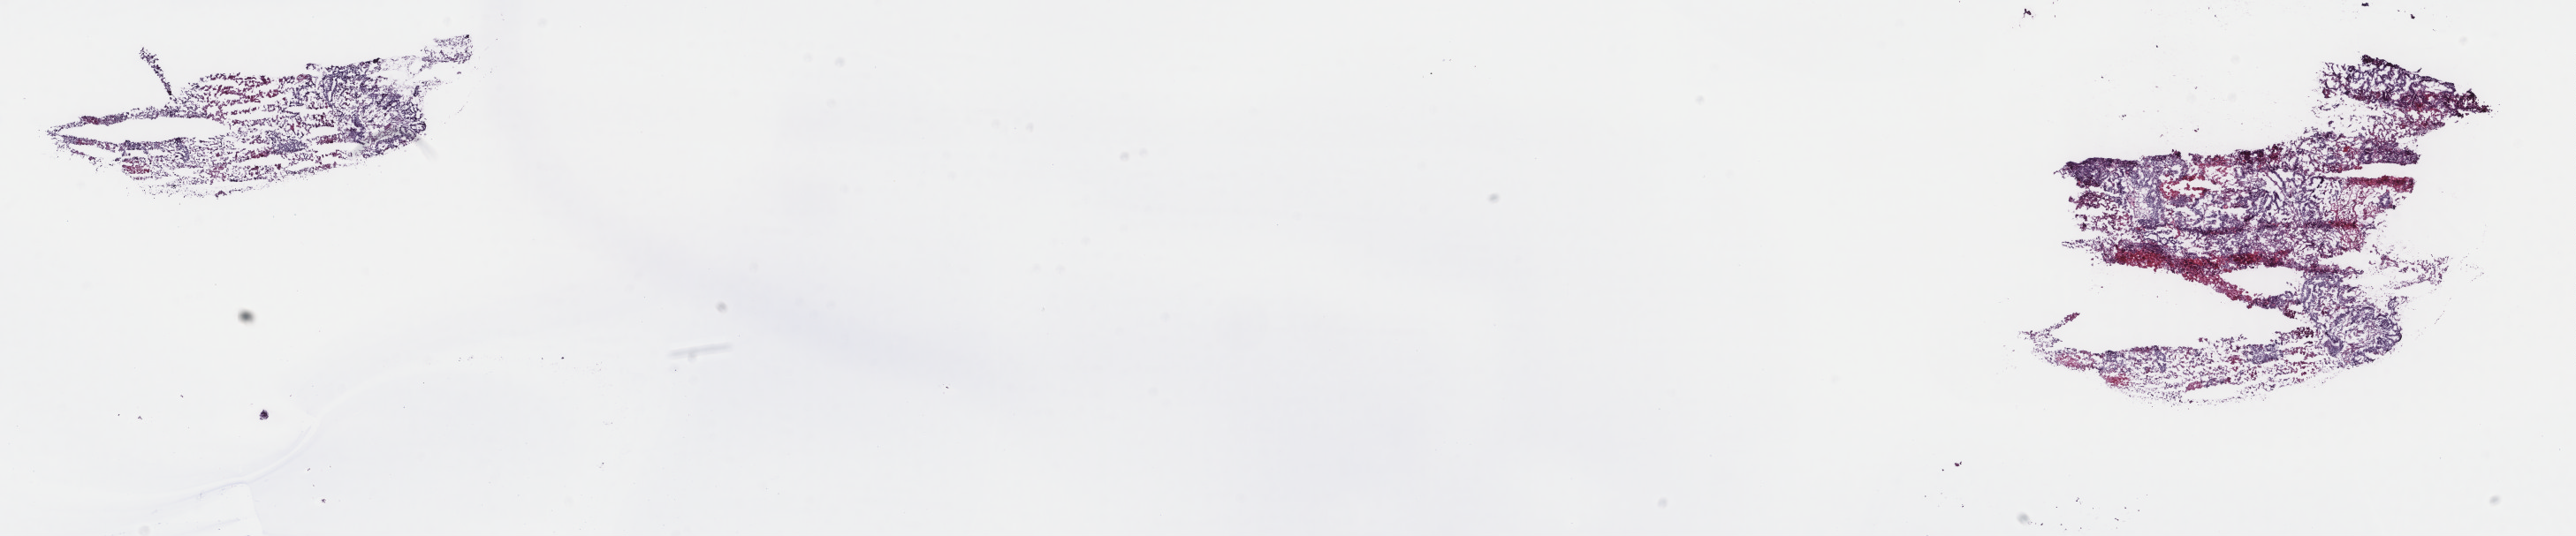
H&E-stained whole-slide image — shown as a low-resolution overview of the whole scanned area (about 23.1 x 4.8 mm, slide scanned at 40x); frozen section from the top of the tissue portion; primary tumour sample from the uterus. Female, age 80 years at initial diagnosis. Histologic grade: G3 (poorly differentiated). Pathologist review of this section (percent, as recorded): tumour cells 85%, tumour nuclei 95%, normal cells 0%, stromal cells 0%, necrosis 15%. Inflammatory infiltration, as recorded: lymphocyte infiltration 1%, monocyte infiltration 1%, neutrophil infiltration 0%.
- FIGO stage: IA
- pathologic diagnosis: Endometrioid adenocarcinoma, NOS (endometrium)